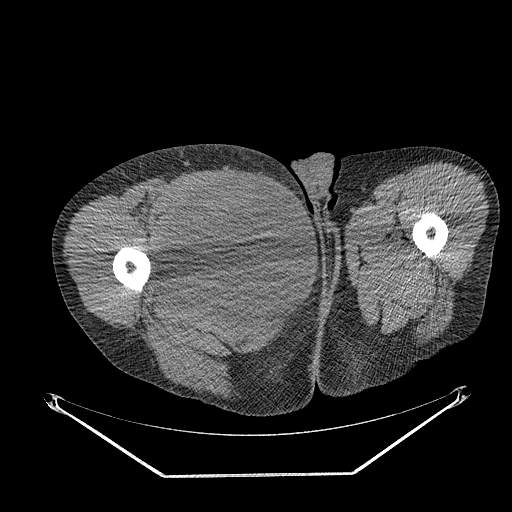
CT of an extremity soft-tissue mass (from a PET/CT study), one axial slice. Position 272 of 311 along the scan axis. Reconstruction kernel STANDARD. 140 kVp. Soft-tissue window (W 400 / L 40 HU). 3.75 mm slice thickness. 512 × 512 image matrix, field of view 500 × 500 mm. Male patient. From the clinical record (not read from this slice): histological type: undifferentiated - pleiomorphic; grade: high; site of the primary tumour: right thigh.
Structures marked on this image (expert contour drawn on MRI and transferred to this co-registered scan by the dataset authors):
- gross tumour volume including surrounding oedema: box from (x=160, y=174) to (x=268, y=279) px
- gross tumour volume (mass): (x=160, y=174)–(x=268, y=279)